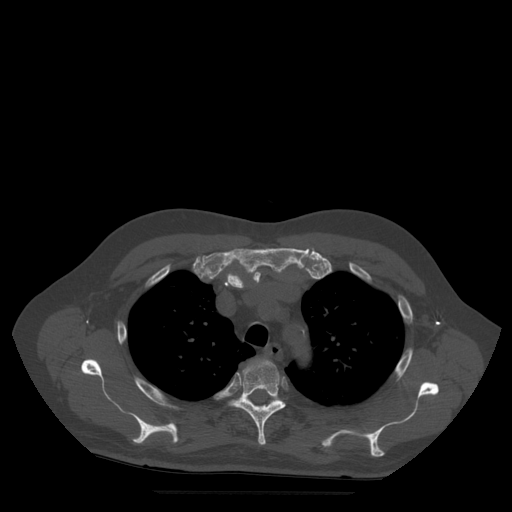
CT including the spine, one axial slice. Position 391 of 522 along the scan axis. Bone window (W 1800 / L 400 HU). 1.25 mm slice thickness. 512 × 512 image matrix. Patient age 72 years. Case-level facts recorded for this patient, not image findings: primary cancer: prostate.
Annotated regions visible in this slice (semi-automatically segmented with operator editing):
- T4 vertebra: bounding box [x1, y1, x2, y2] px = [230, 359, 286, 446]
- T5 vertebra: [245, 397, 279, 406]